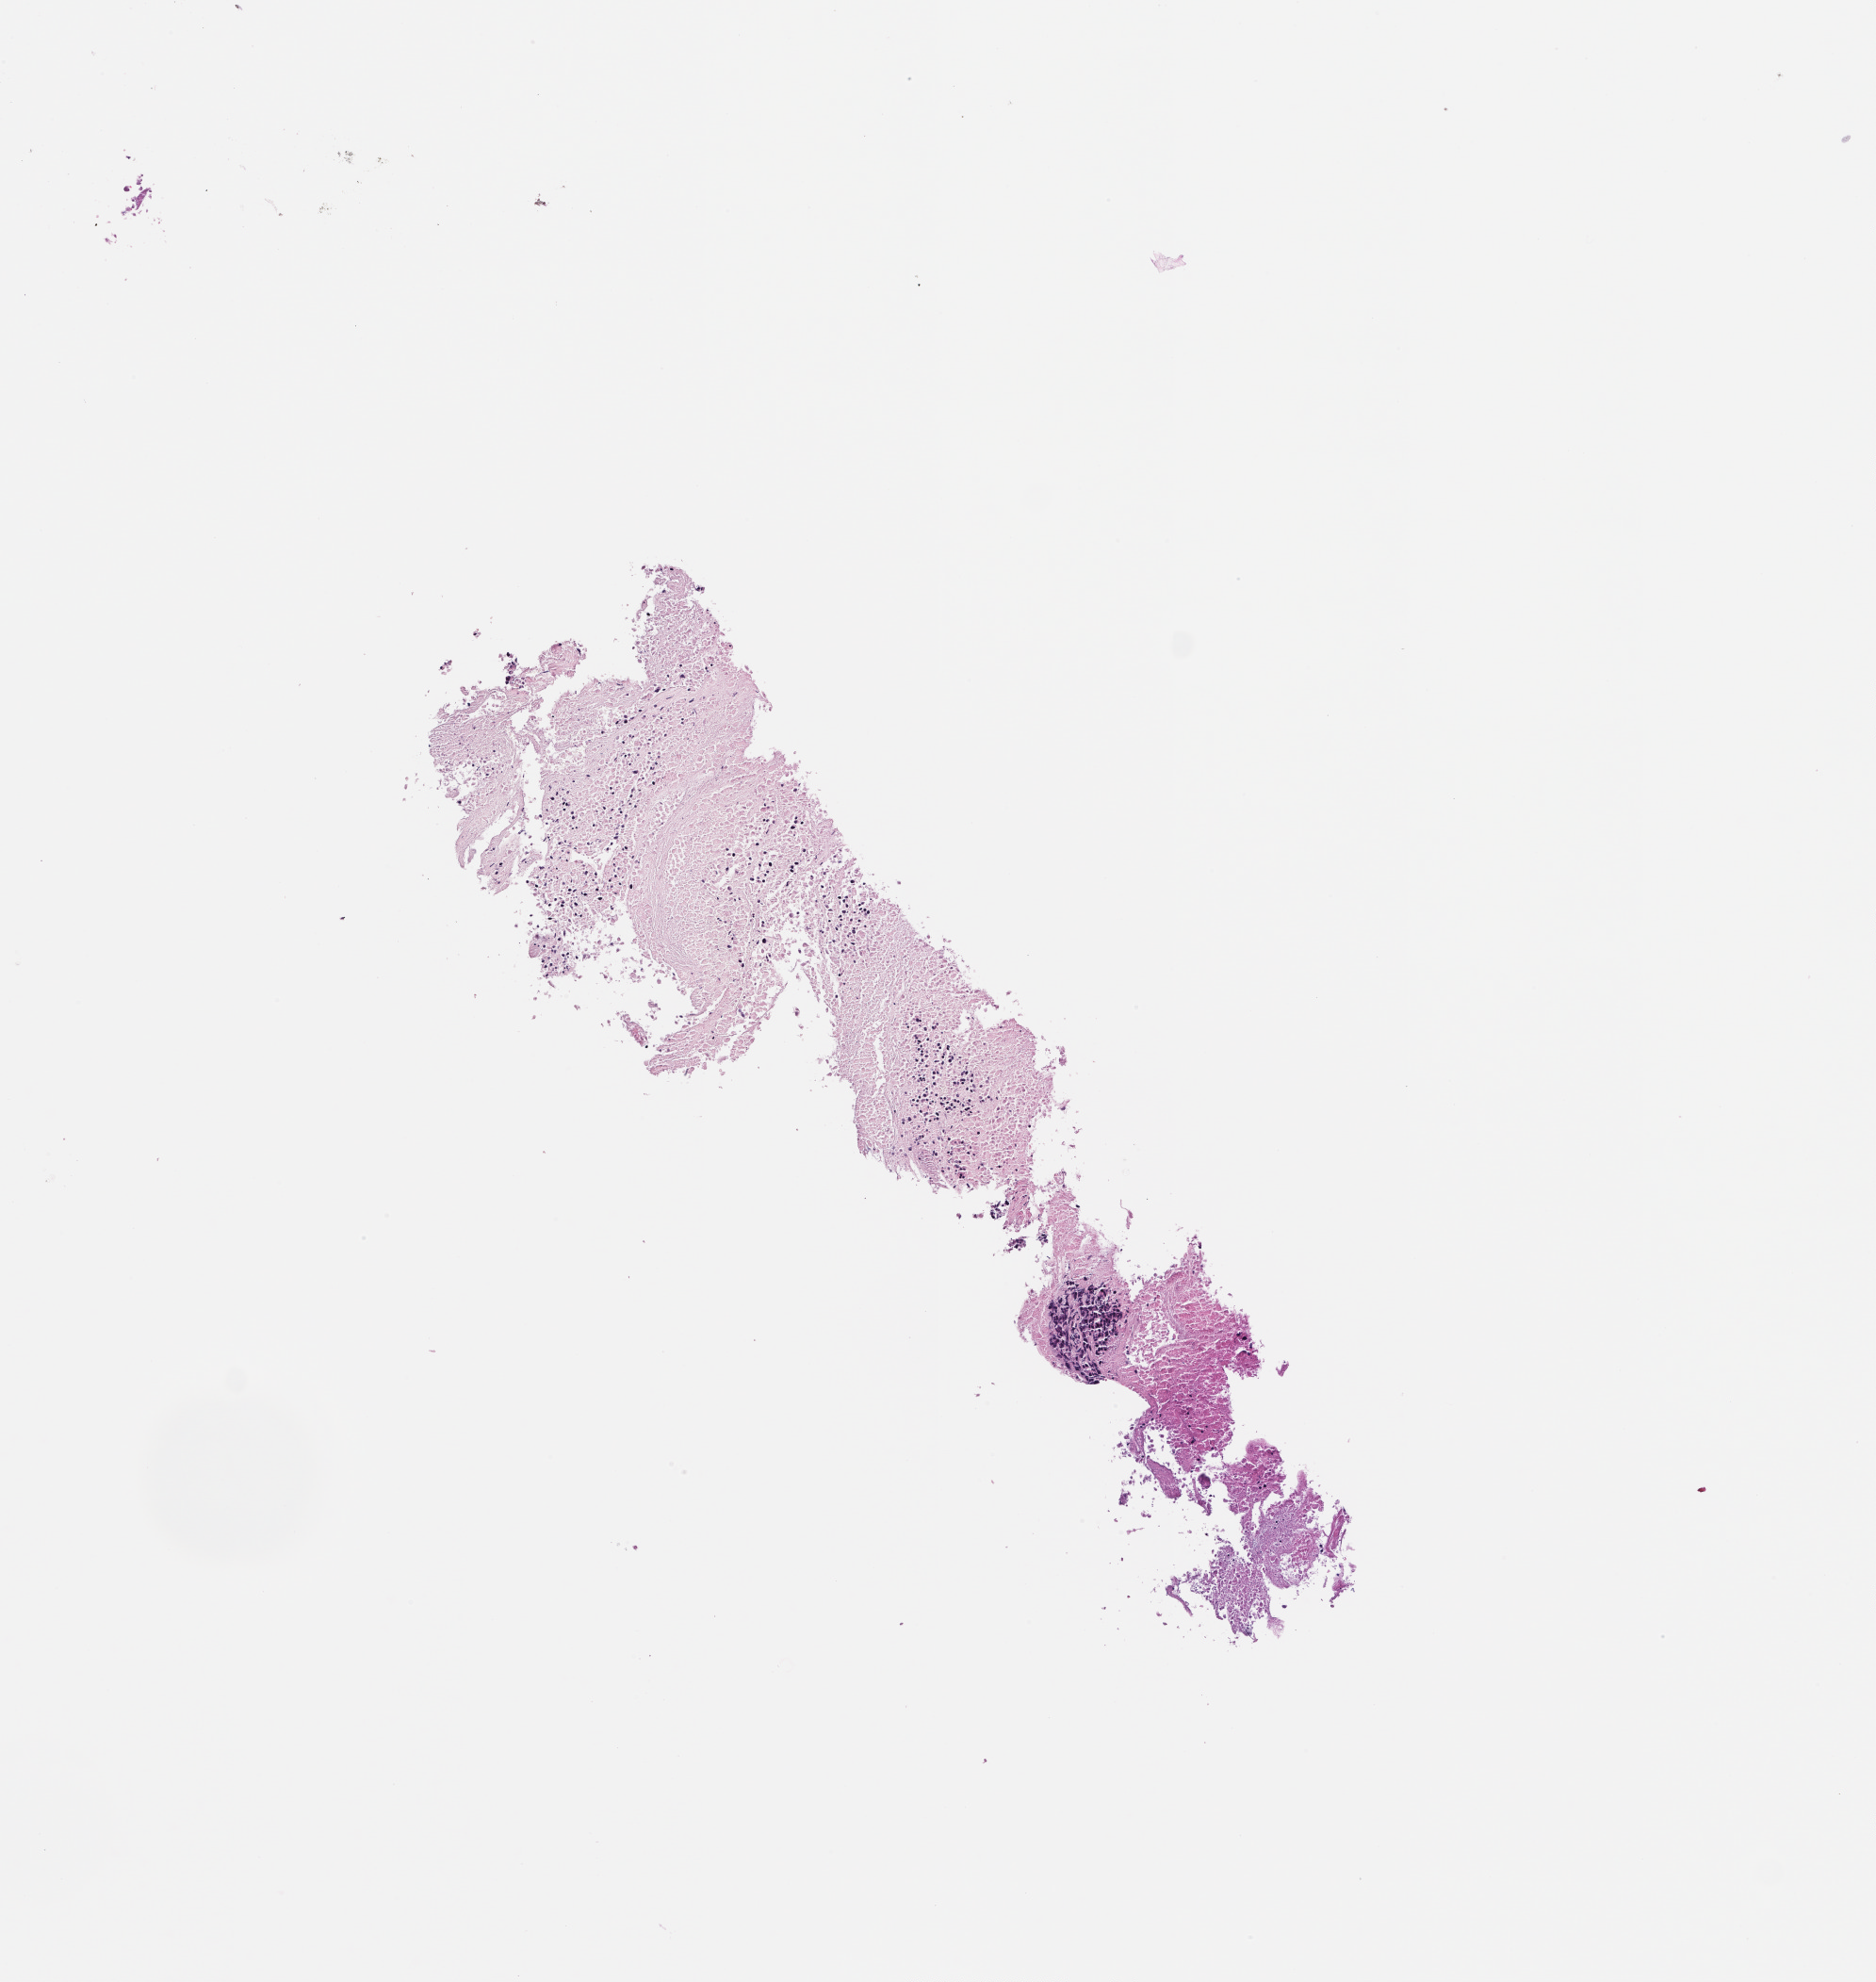
Digitized haematoxylin and eosin-stained section — shown as a low-resolution overview of the whole scanned area (about 4.0 x 4.2 mm); formalin-fixed paraffin-embedded section. Female patient.
This section: metastatic tumor tissue. Patient diagnosis (primary): Colorectal Carcinoma.